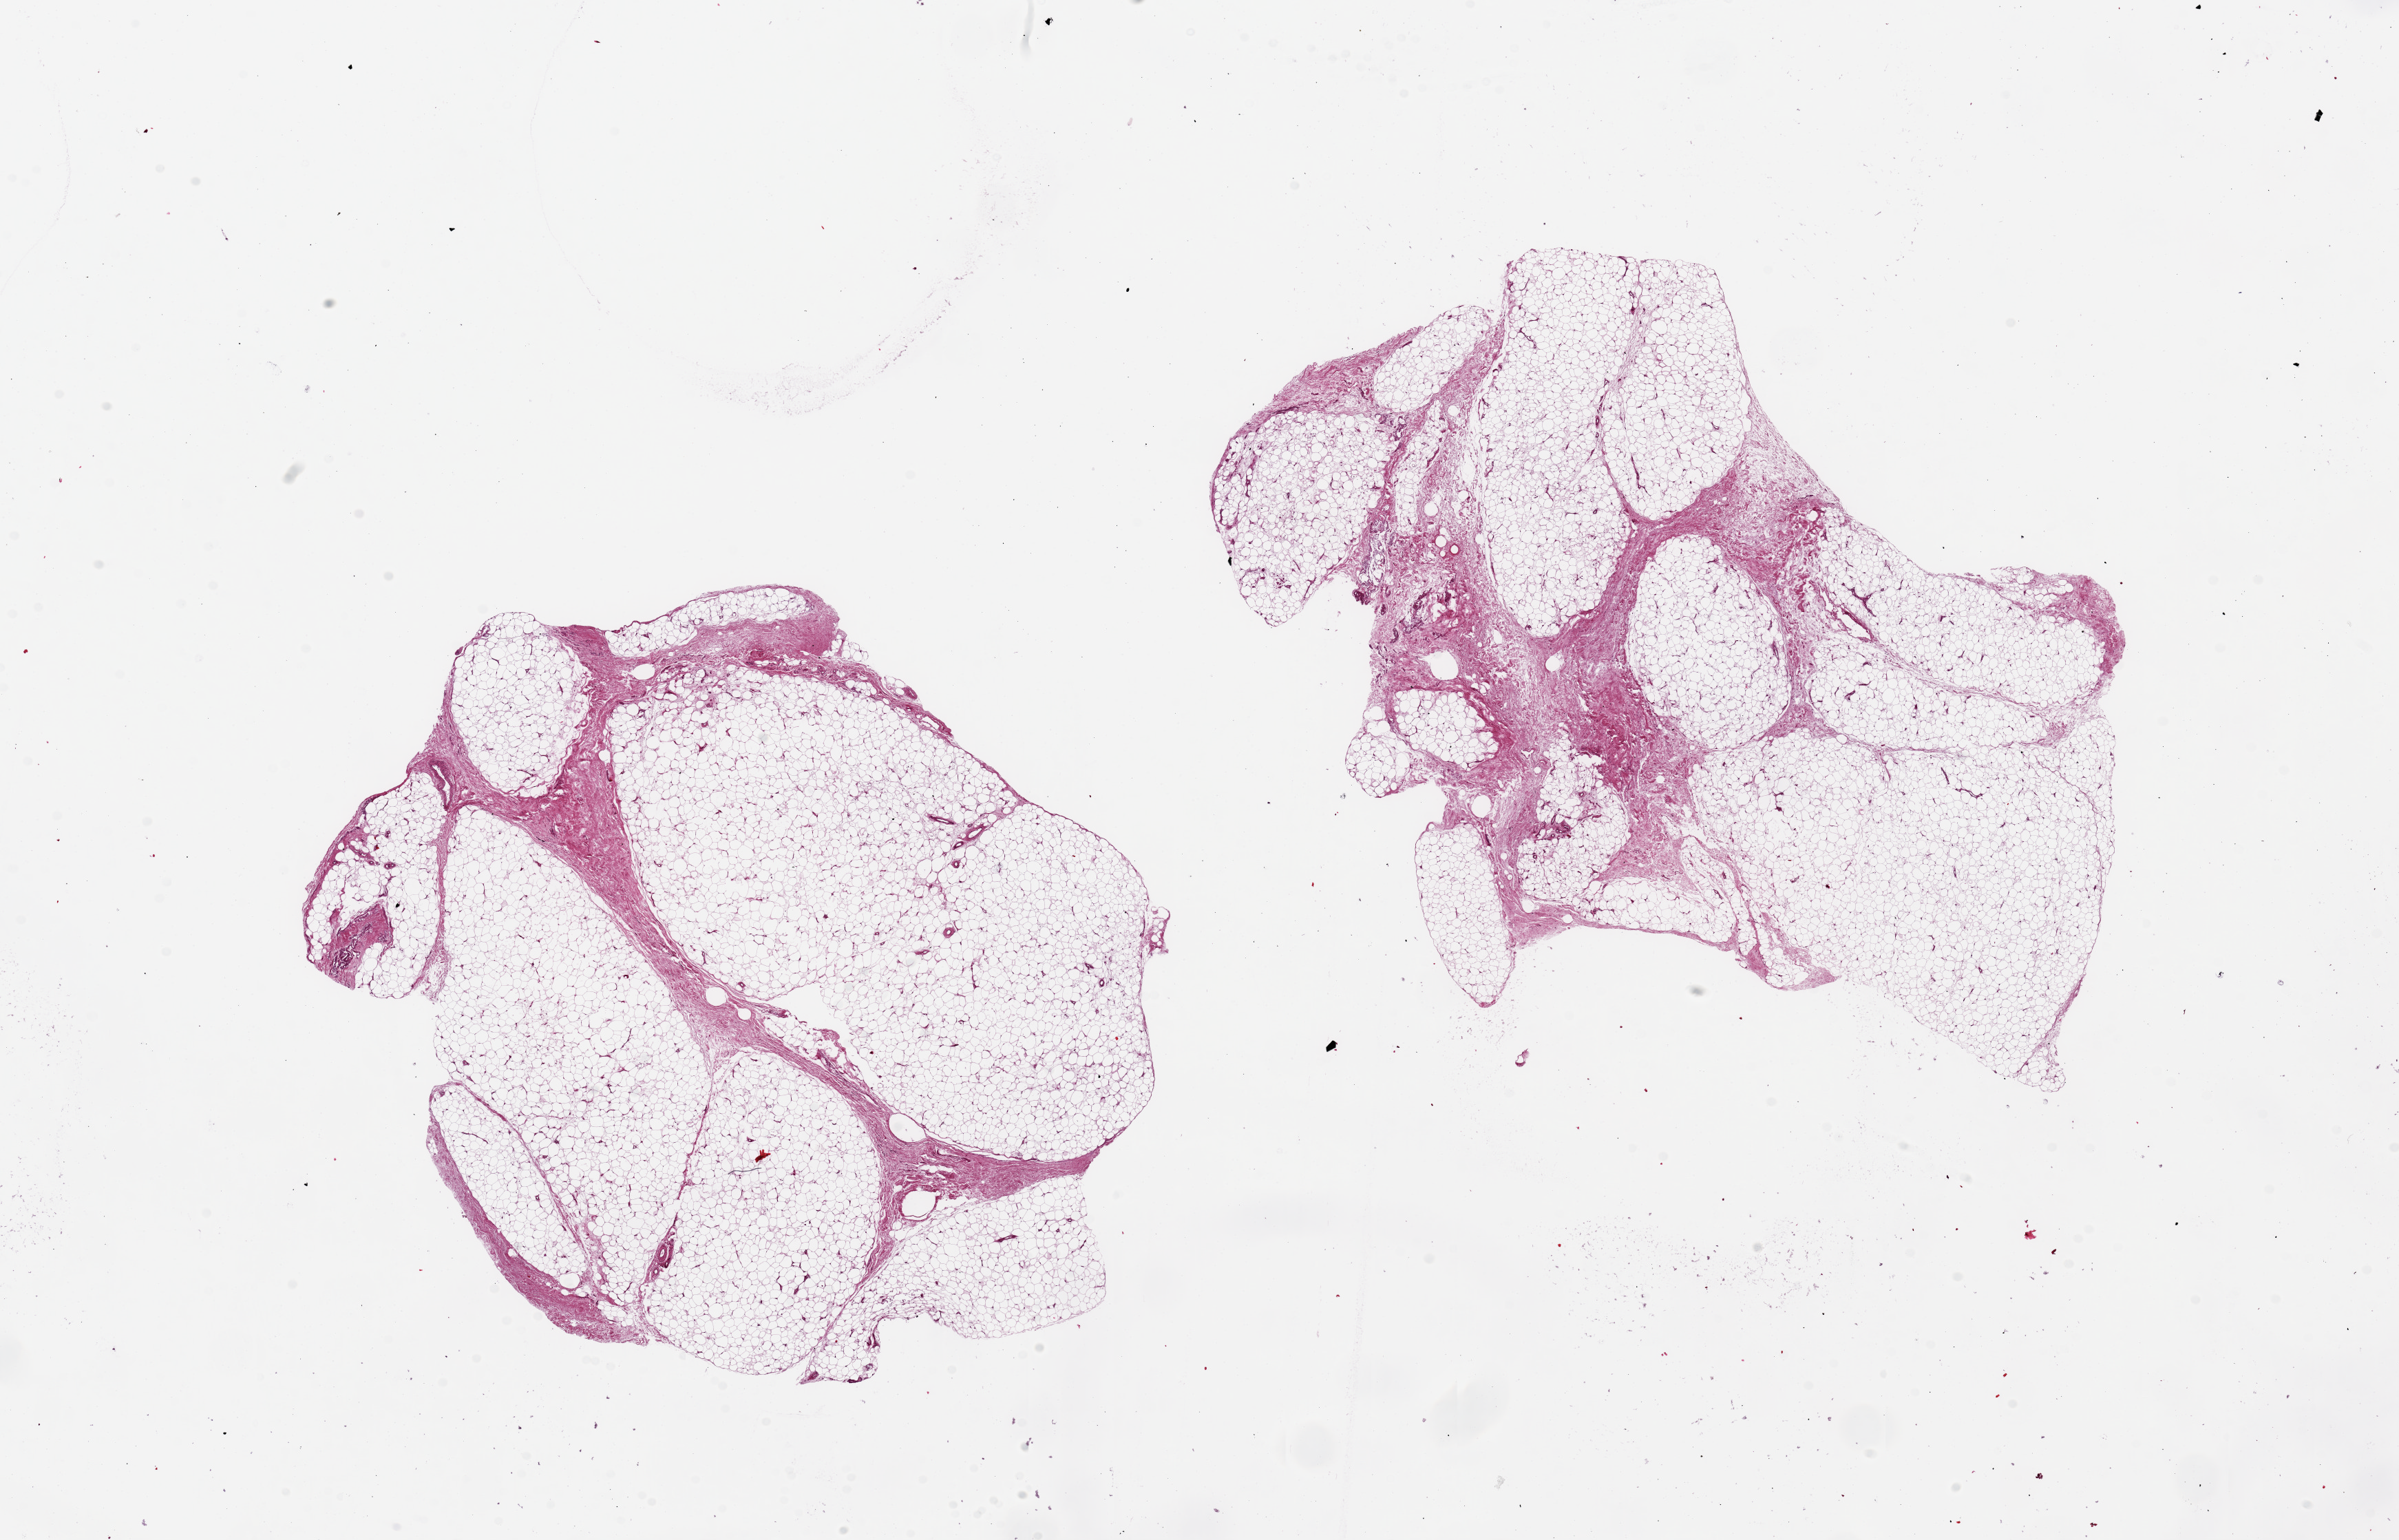
Whole-slide image, haematoxylin and eosin stain, whole scanned area (about 27.6 x 17.7 mm, slide scanned at 20x) shown as a low-resolution overview; PAXgene-fixed paraffin-embedded (PFPE) section; target tissue: adipose tissue; donor tissue sample. Donor: male.
- pathologist's review note for this sample: 2 pieces ~10x7mm; Fibrous areas in both ~15% total area